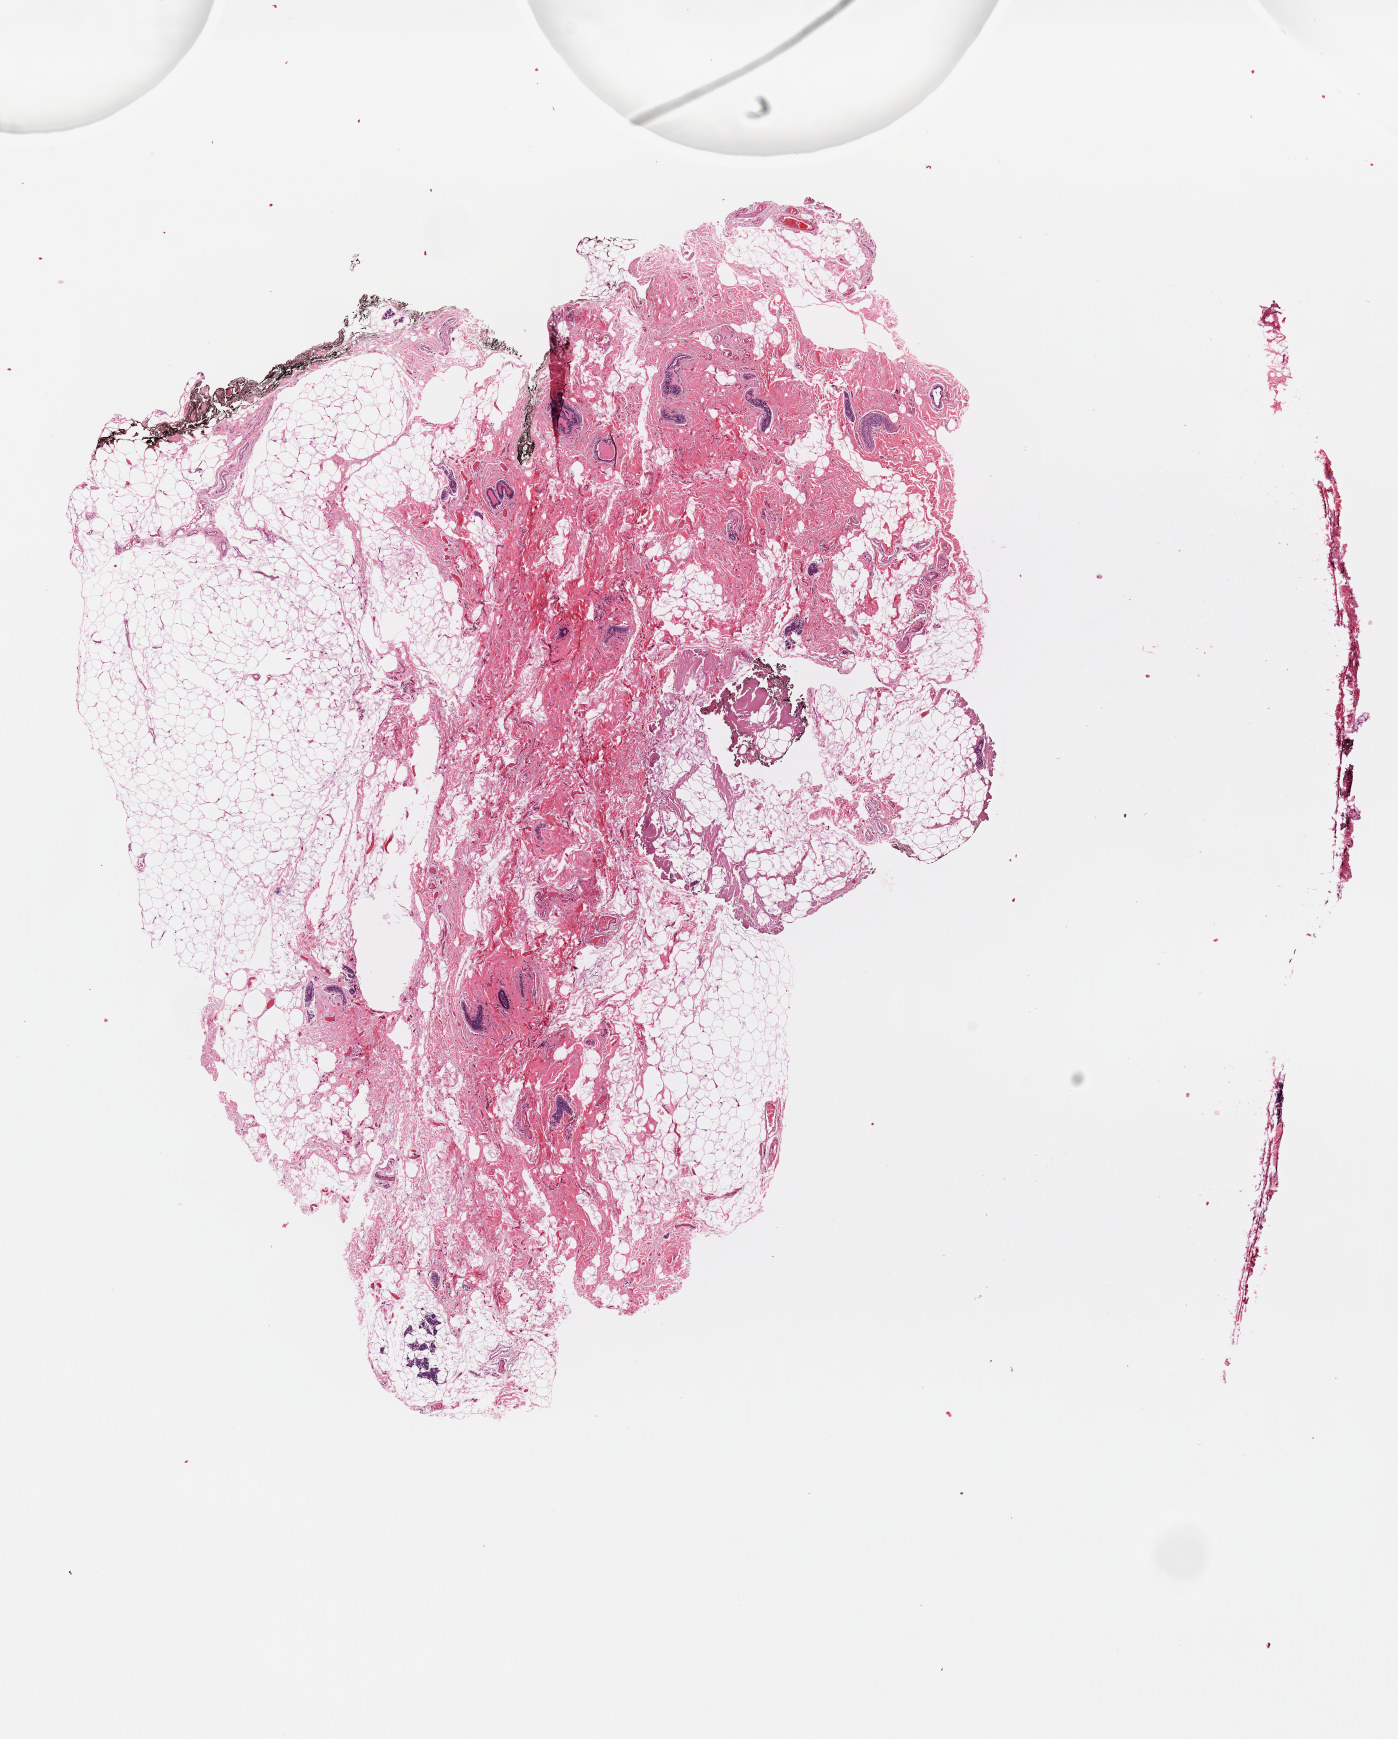
Whole-slide histology image, H&E-stained — low-resolution overview of the scanned area, about 11.0 x 13.7 mm (from a 40x scan); FFPE section; primary tumour sample from the breast. Female, age 58 years at initial diagnosis.
Diagnosis: Infiltrating duct carcinoma, NOS.